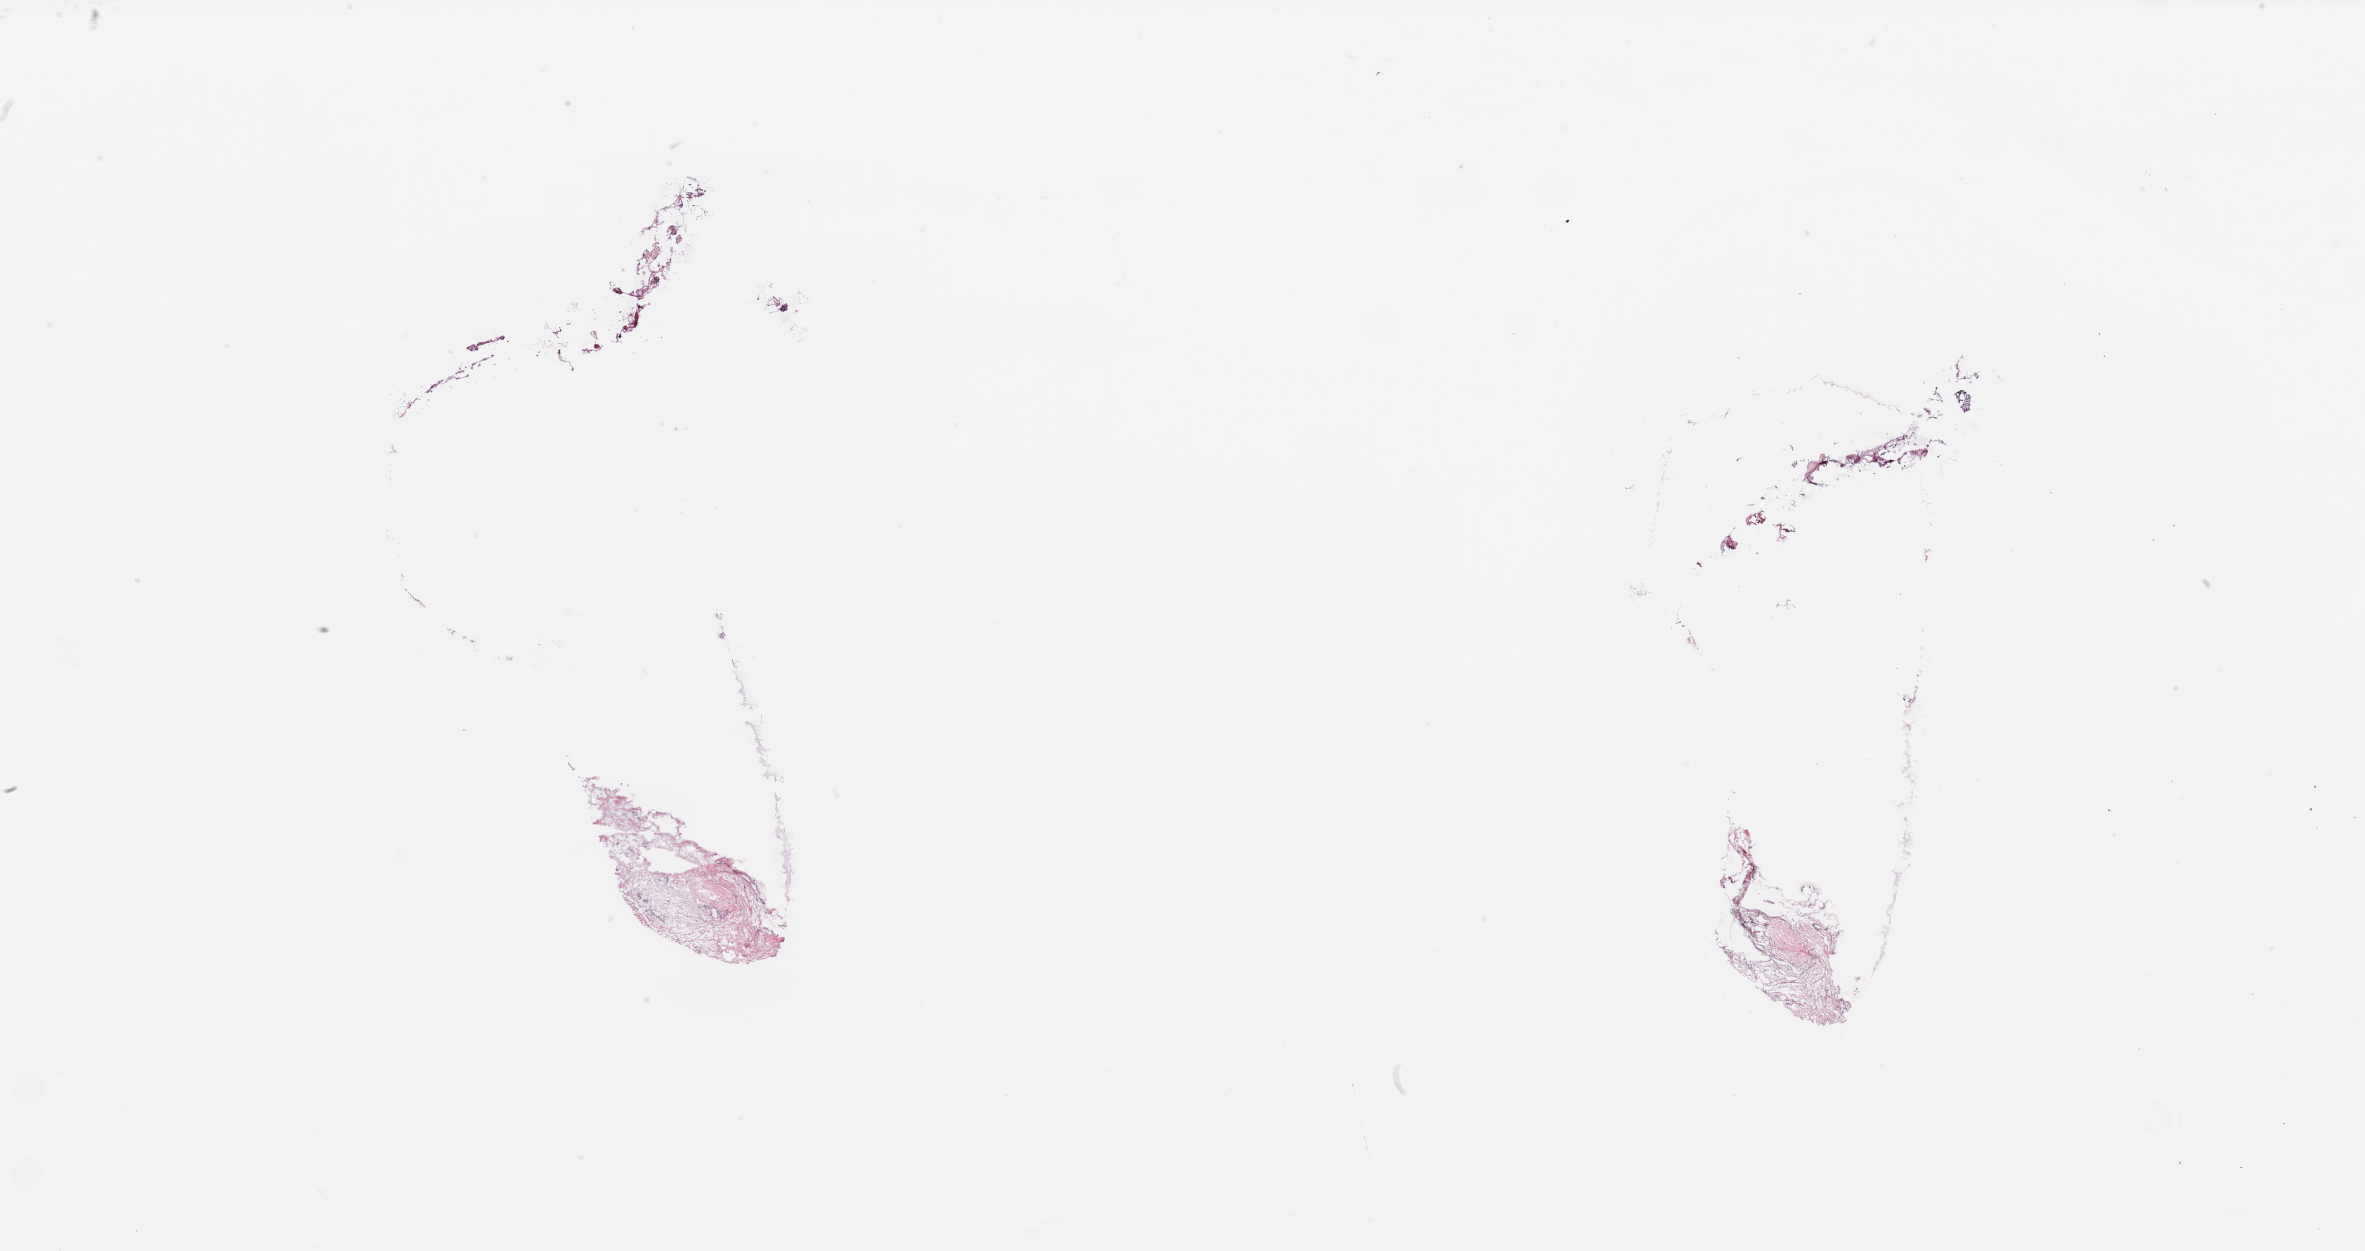
H&E whole-slide image, low-resolution overview of the scanned area, about 37.4 x 19.8 mm (slide scanned at 20x). Breast, tissue type not recorded.
Patient diagnosis (cohort enrolment): breast cancer (breast).